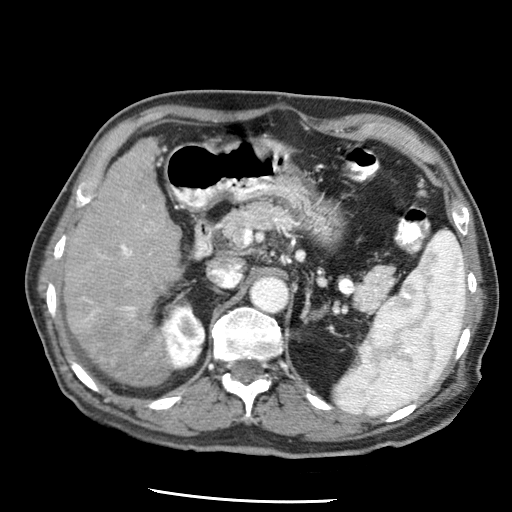
Contrast-enhanced abdominal CT (liver protocol), one axial slice; position 26 of 79 along the scan axis; reconstruction kernel STANDARD; soft-tissue window (W 400 / L 40 HU); 2.5 mm slice thickness; 512 × 512 image matrix, field of view 320 × 320 mm. Case-level facts recorded for this patient, not image findings: diagnosis: hepatocellular carcinoma (patient treated with transarterial chemoembolisation; whether this scan precedes or follows treatment is not stated here); TNM stage (as recorded): Stage-IIIA; Child-Pugh class: A; tumour differentiation: moderately differentiated; tumour nodularity: multinodular.
Annotated regions visible in this slice (semi-automatically segmented with operator editing):
- liver parenchyma outside the tumour (the mass and vessels are separate outlines, so this box may not span the whole liver): bounding box (x1, y1, x2, y2) in pixels: (62, 138, 180, 382)
- liver vessels: (83, 205, 152, 322)